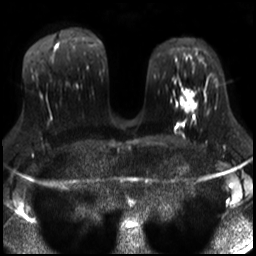
Breast MRI, one axial slice. Slice 16 of 30 in the series (ordered by position). Diffusion-weighted series; image 2 of 4 stored at this slice position (different b-values; order by instance number). 3 T. 4 mm slice thickness. 256 × 256 image matrix, field of view 320 × 320 mm. Female patient.
Outlined on this slice (outlined manually by an expert reader):
- tumour on diffusion-weighted imaging: bounding box [x1, y1, x2, y2] px = [180, 89, 194, 112]